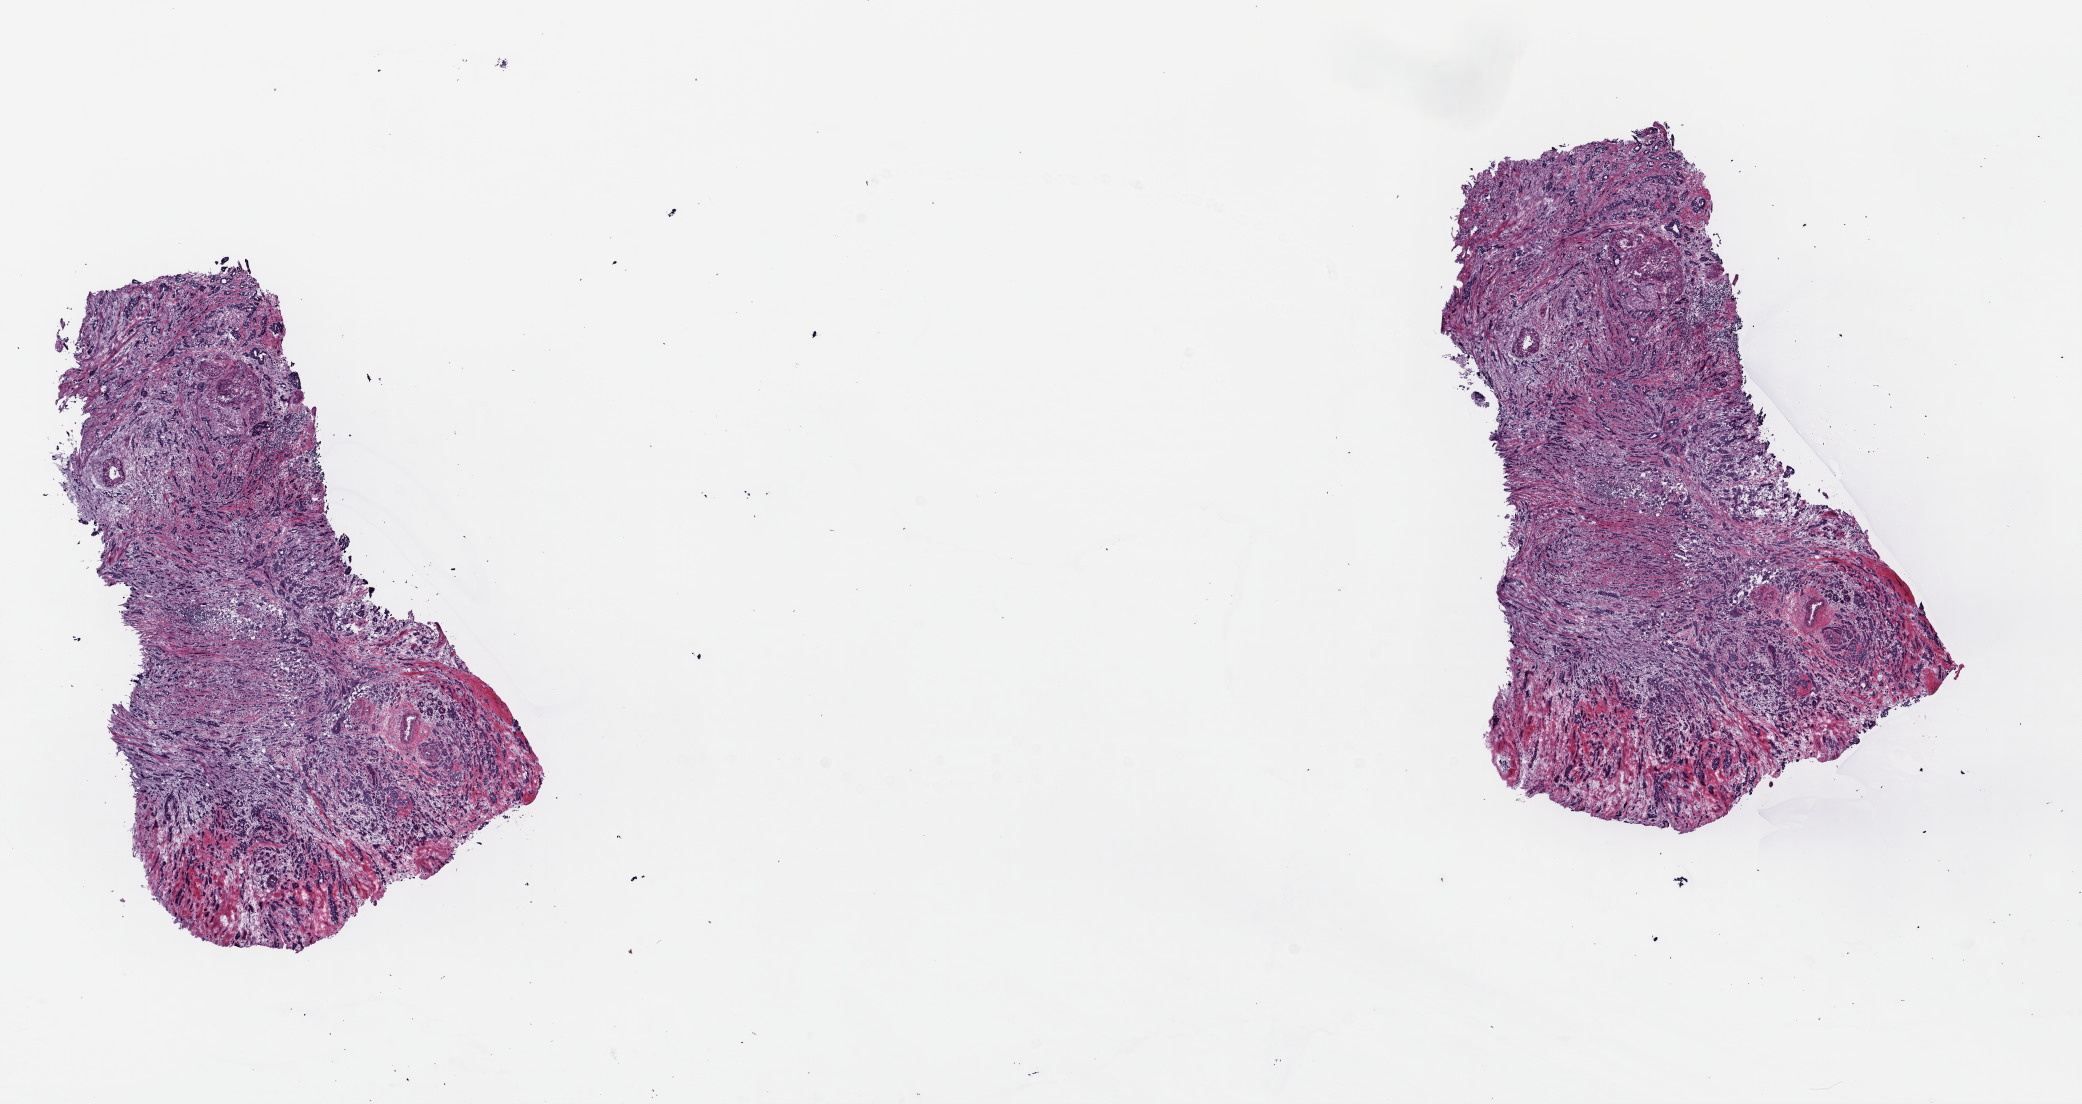
Whole-slide histology image, Hematoxylin and eosin (H&E) stained, low-resolution overview of the scanned area, about 16.4 x 8.7 mm (from a 40x scan); frozen section from the top of the tissue portion; breast, primary tumour sample. Patient: female, age at initial diagnosis 62 years. Pathologist review of this section (percent, as recorded): tumour cells 100%, tumour nuclei 70%, normal cells 0%, stromal cells 0%, necrosis 0%. Inflammatory infiltration, as recorded: lymphocyte infiltration 0%, monocyte infiltration 0%, neutrophil infiltration 0%.
AJCC pathologic stage: IIB (7th edition). Laterality: right. Pathologic diagnosis: Infiltrating duct carcinoma, NOS.